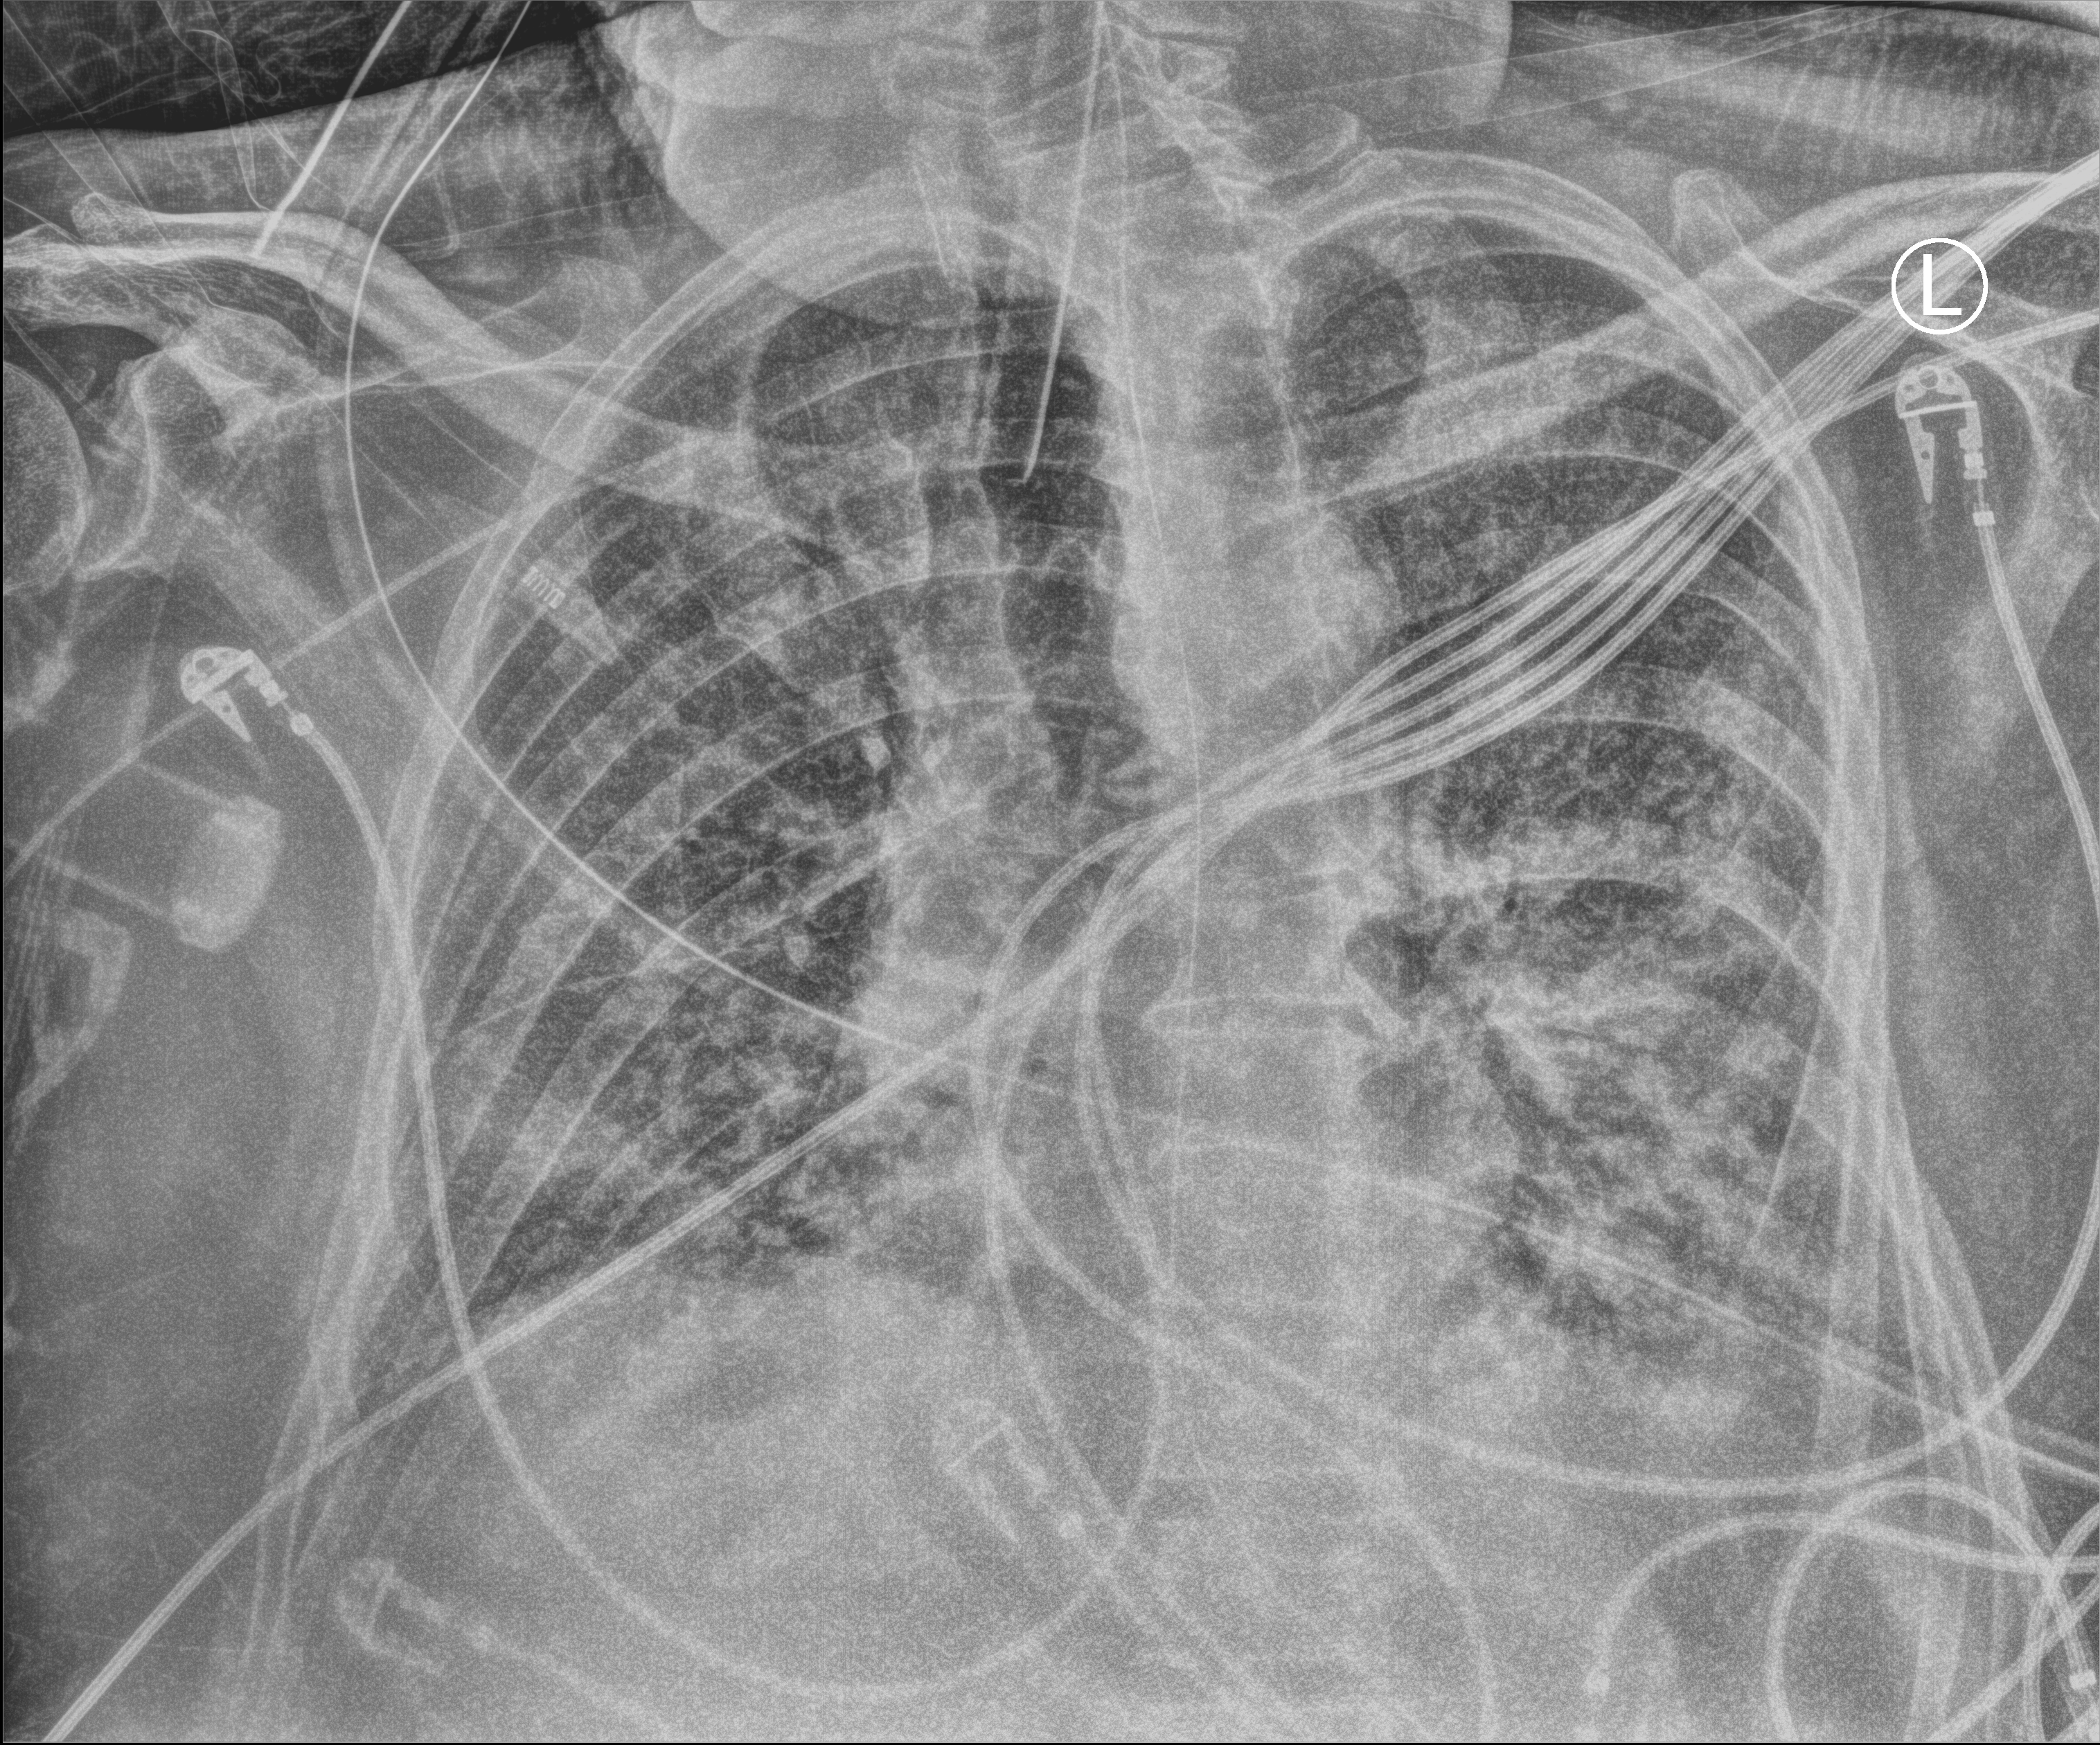
Portable chest radiograph. Patient hospitalised with COVID-19; male, aged 60–74 years.
From the hospital-stay record, not from the radiograph (when in the stay this image was taken is not recorded): diabetes (admission record): no; chronic kidney disease (admission record): no.